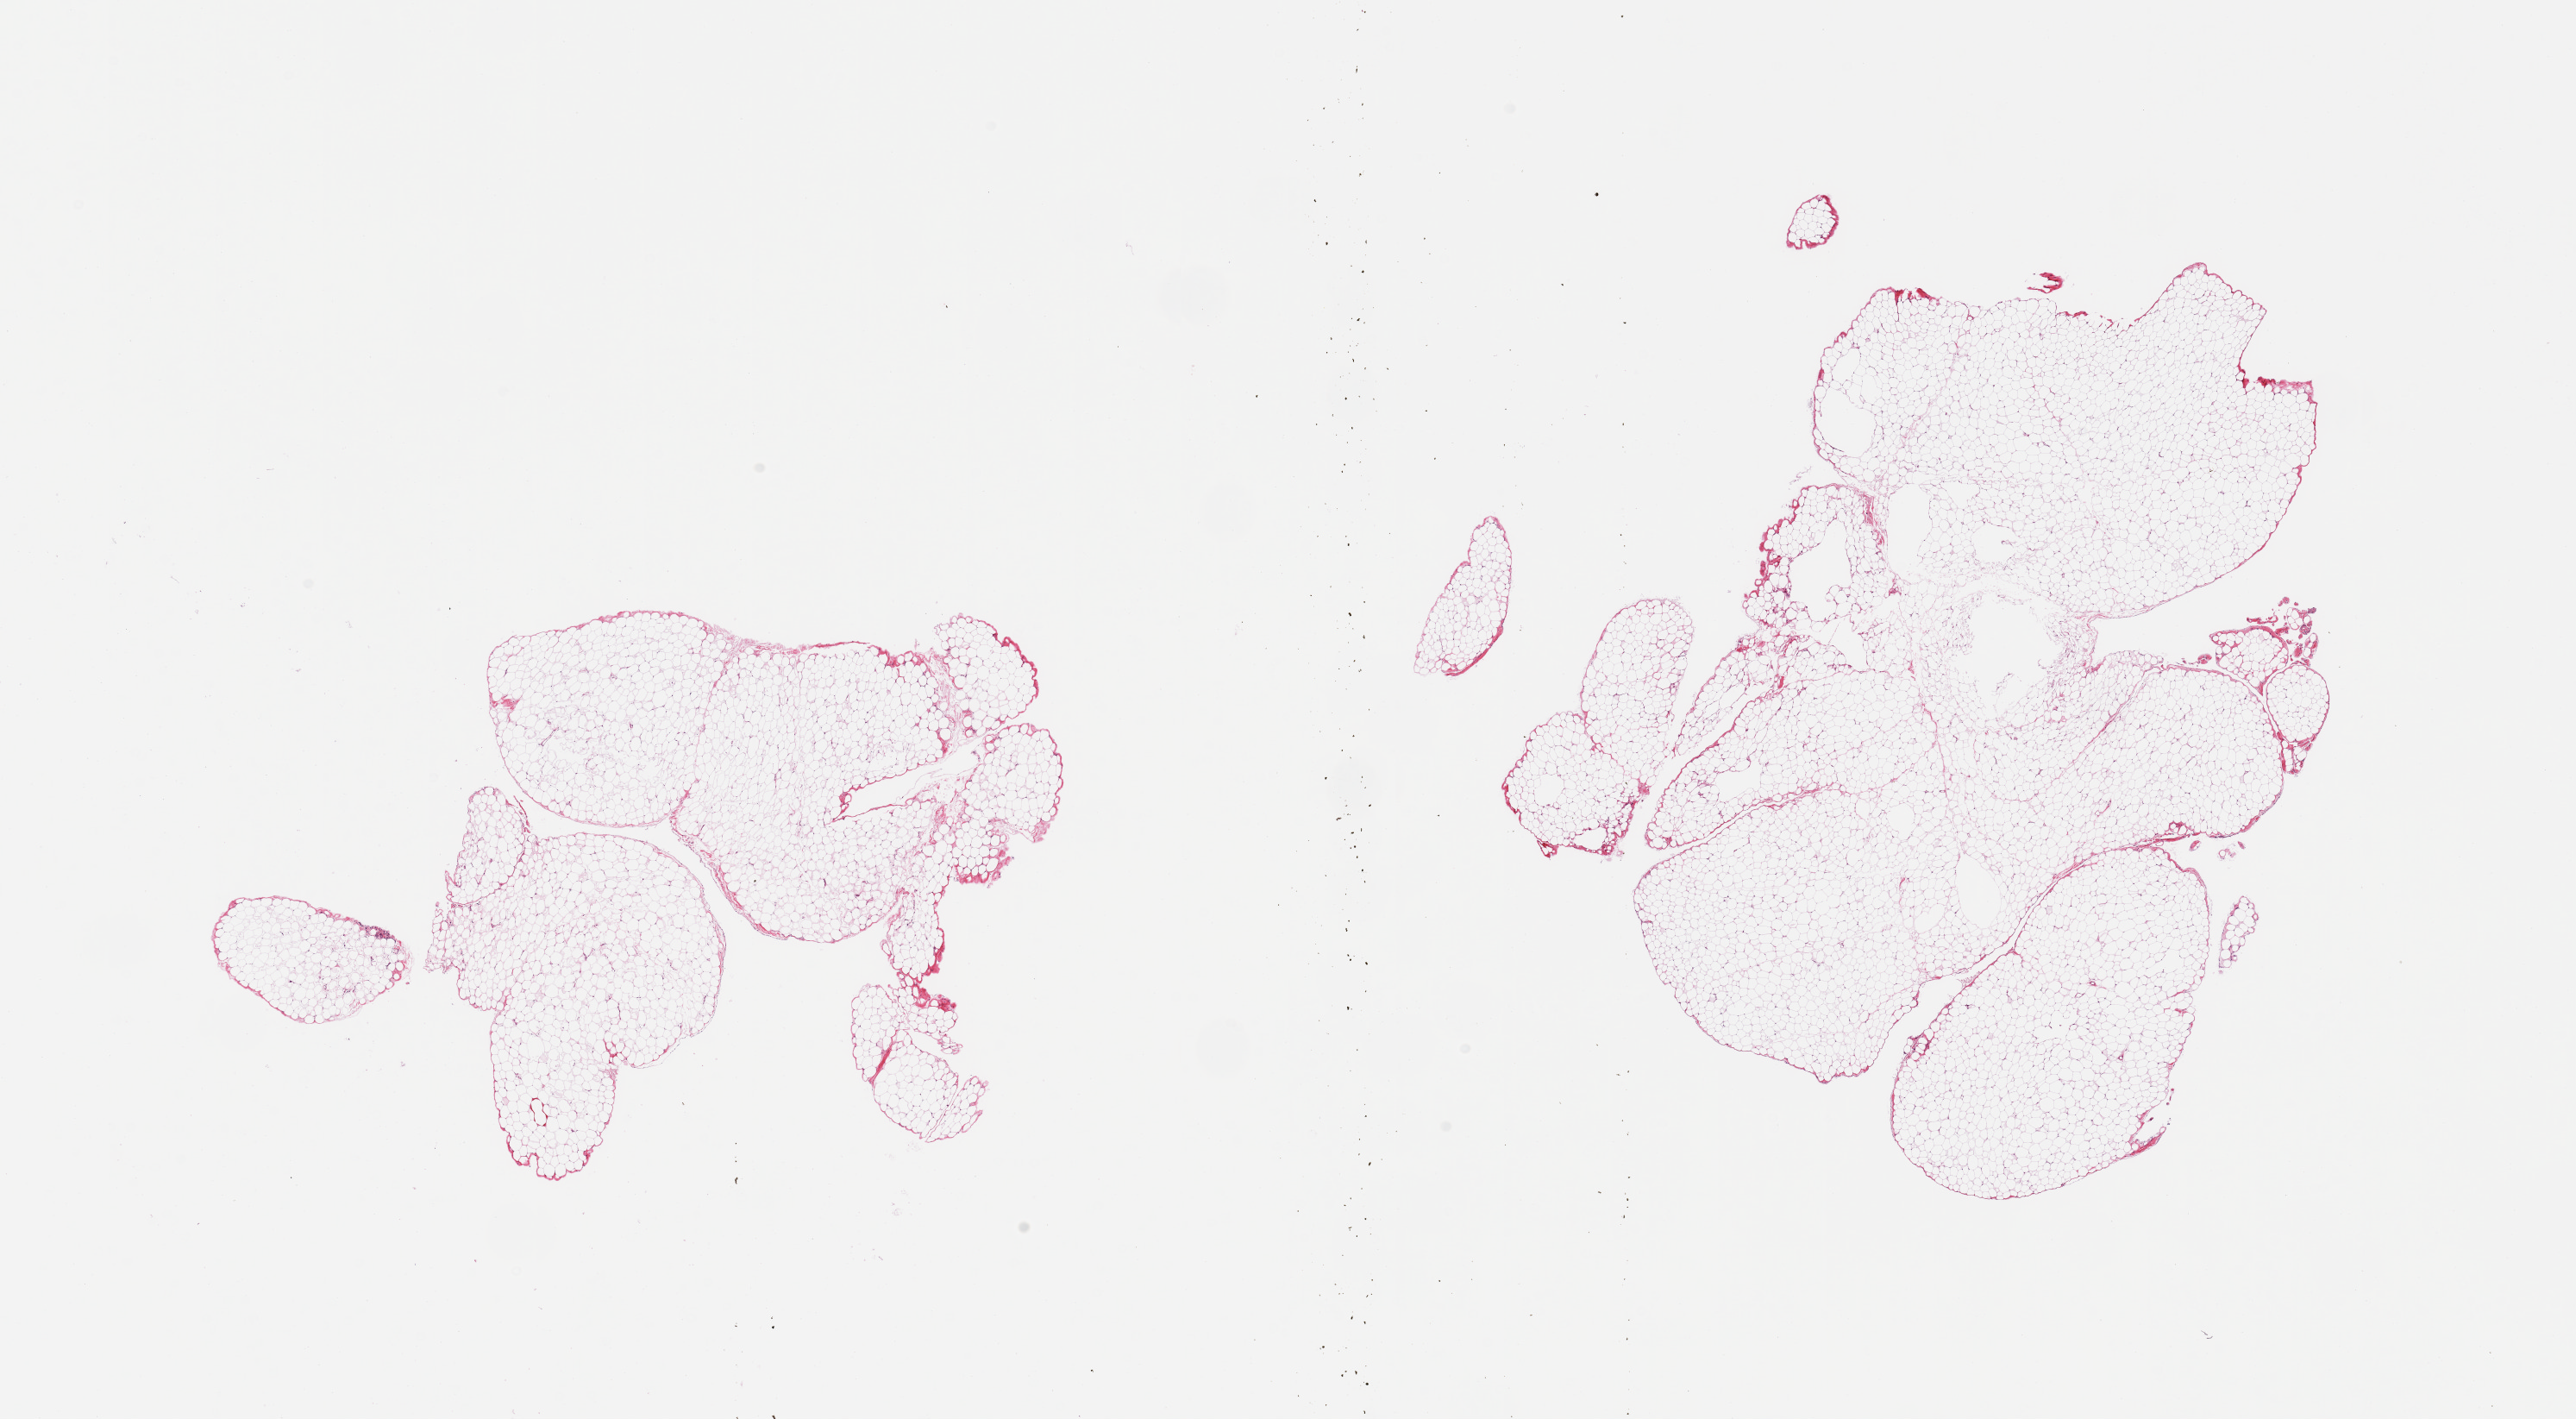
H&E whole-slide image, brightfield — shown as a low-resolution overview of the whole scanned area (about 23.6 x 13.0 mm, acquisition: 20x scan), PAXgene-fixed paraffin-embedded (PFPE) section, section of omentum (target tissue), tissue donor sample. Male donor.
Review note (as recorded): 2 pieces; lobulated mature fat.